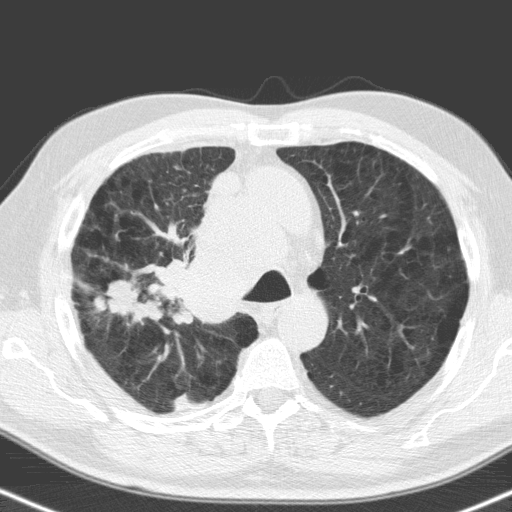
Axial slice from a low-dose chest CT screening exam; first (baseline) screen; lung window (W 1500 / L -600 HU); 3.2 mm slice thickness; 120 kVp. Male, age 71 years at enrolment.
Lesion marked by an expert reader, box from (x=93, y=272) to (x=172, y=336) px. The screening reader recorded 2 non-calcified nodules or masses ≥4 mm on this exam (right upper lobe, right upper lobe); which of them this box marks is not recorded. Later outcome: lung cancer diagnosed 31 days after this screen — small cell carcinoma, NOS, right upper lobe, stage IV (AJCC 6th edition), 40 mm at pathology.